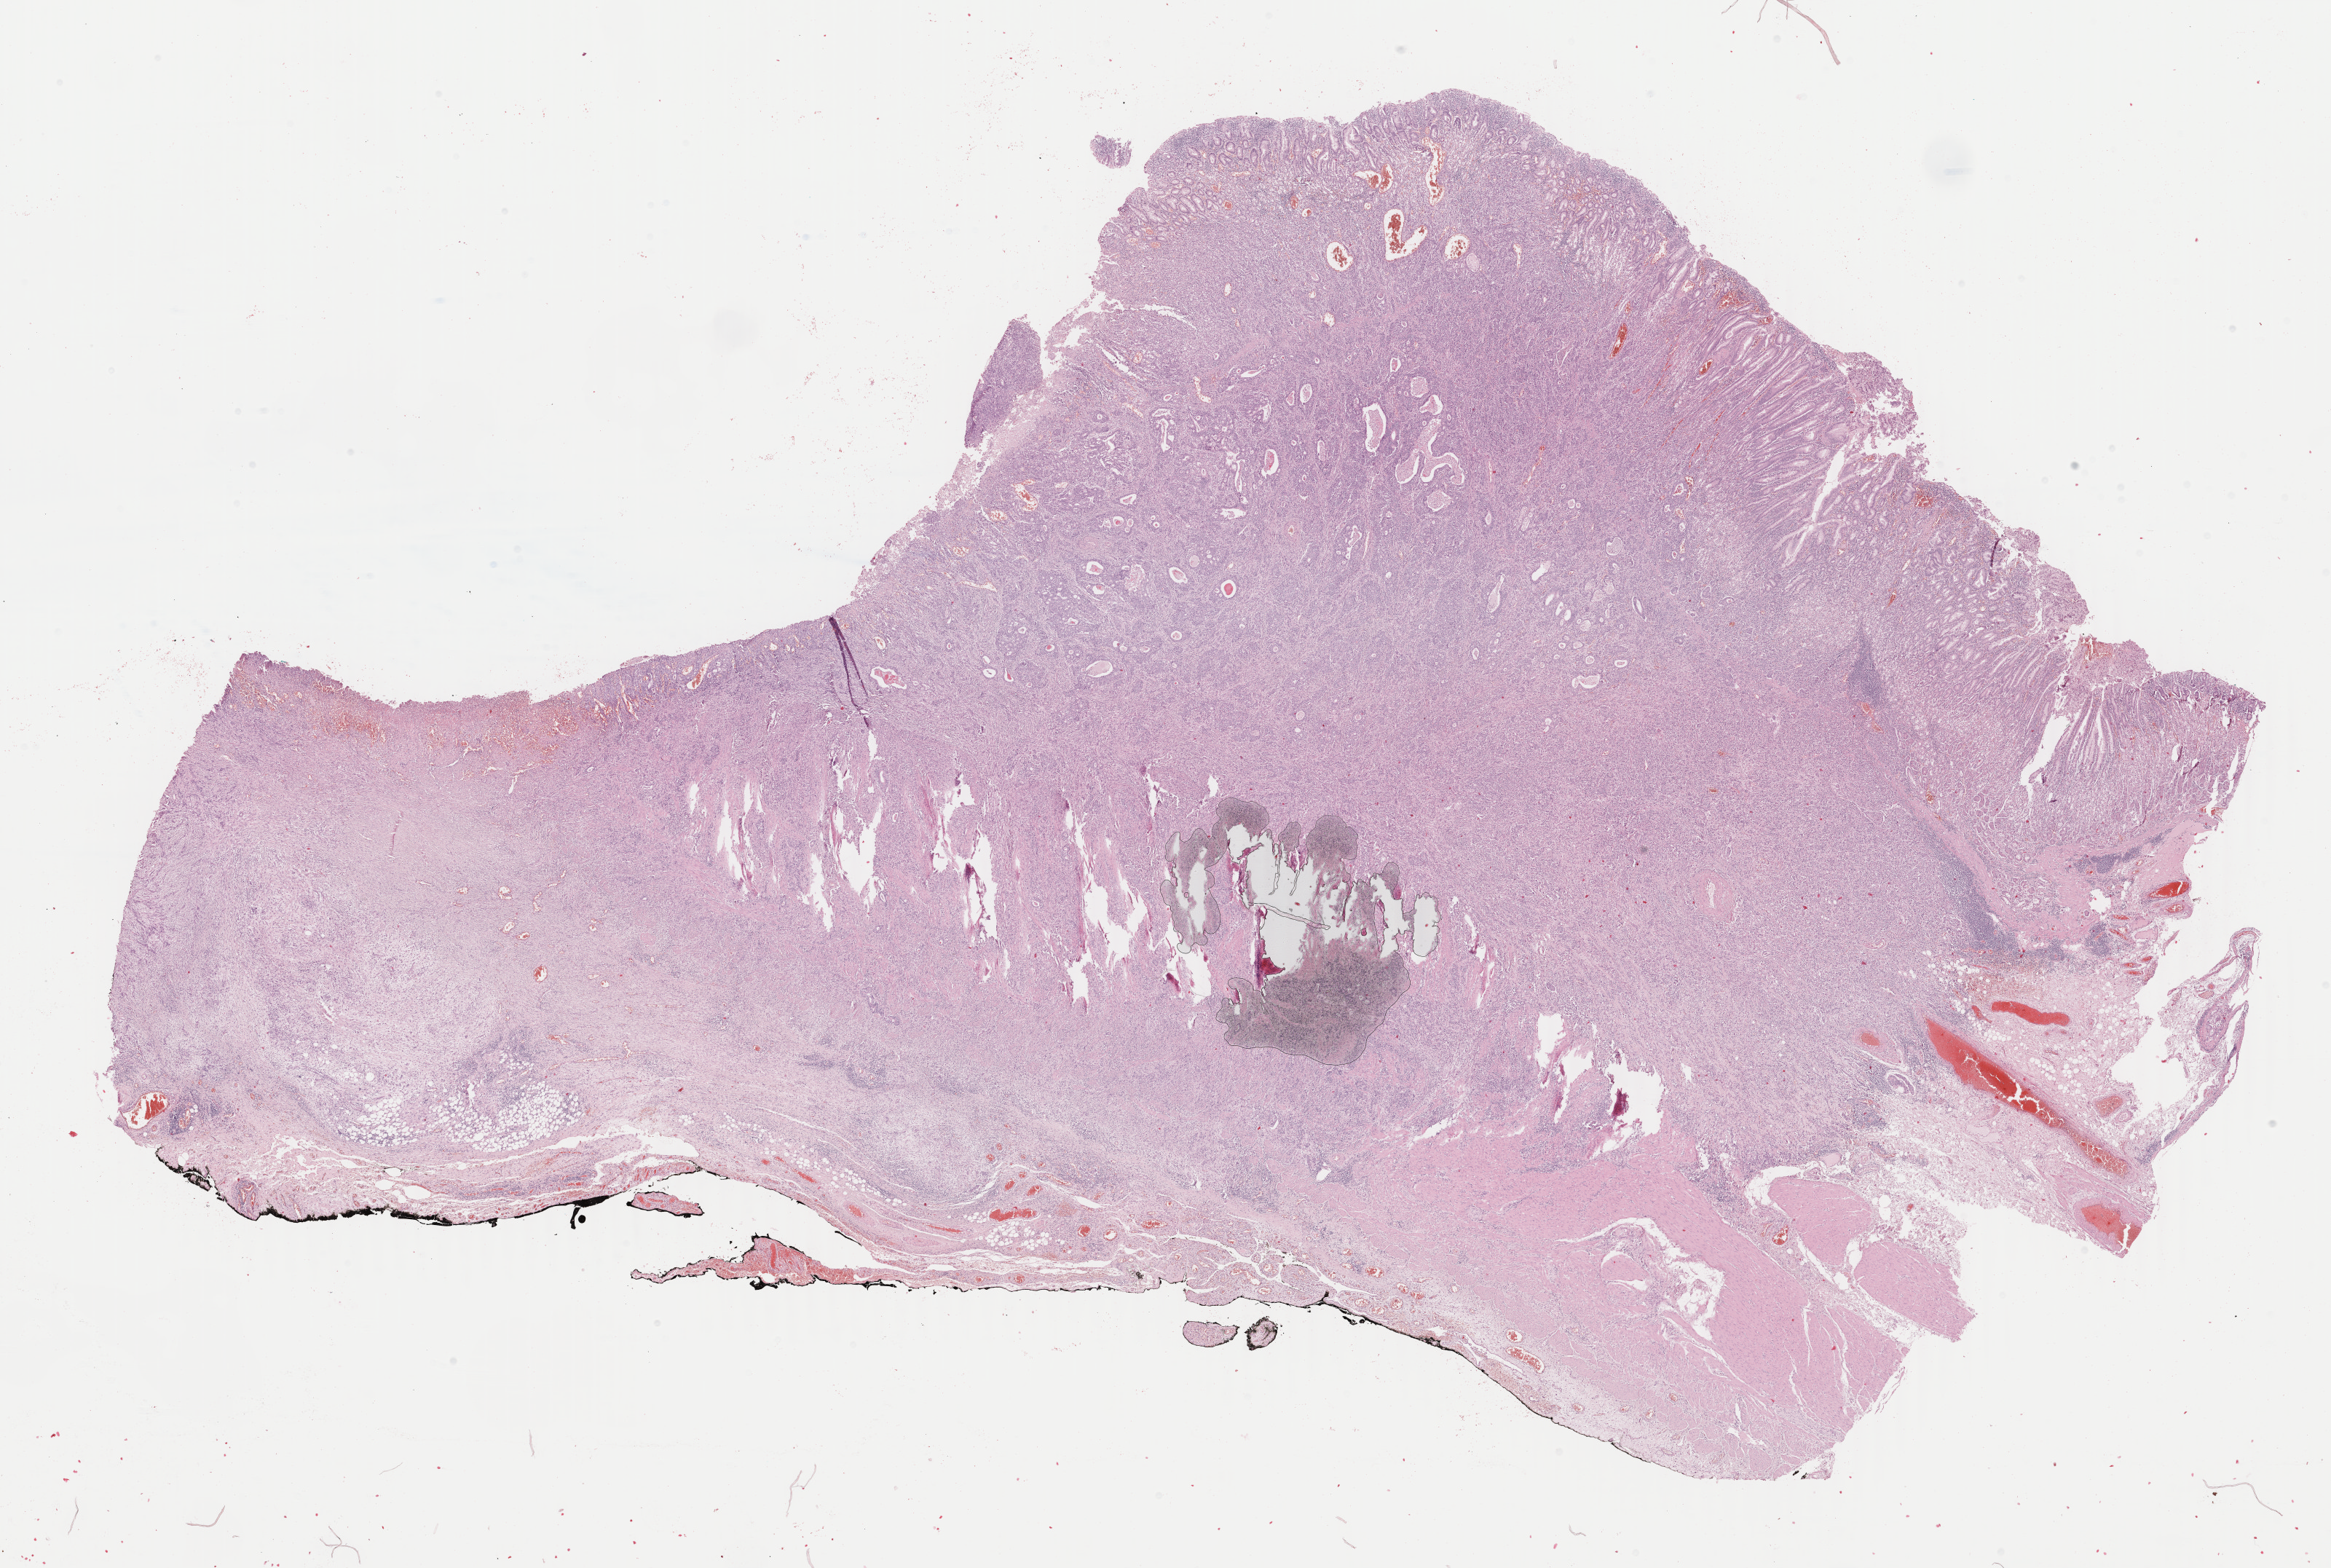
Whole-slide histology image, H&E-stained — whole scanned area (about 25.5 x 17.1 mm, from a 40x scan) shown as a low-resolution overview. FFPE section. Stomach, primary tumour sample. Female patient; age at initial diagnosis 53 years.
Pathologic diagnosis: Tubular adenocarcinoma (cardia, NOS).